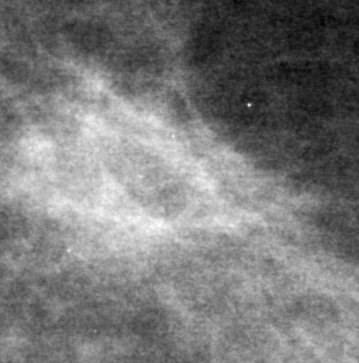
Region of interest cut from a scanned film mammogram (one marked finding), left breast, CC view, BI-RADS breast density category 2 (scale 1–4).
- Mass, shape irregular, margins ill defined; BI-RADS assessment category 2; subtlety rating 3 on a 1 (subtle) to 5 (obvious) scale; pathology (as recorded): benign.